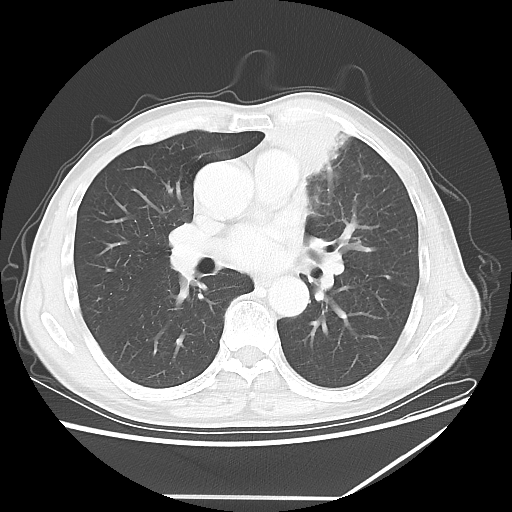
Chest CT, one axial slice; position 33 of 64 along the scan axis; 100 kVp; lung window (W 1500 / L -600 HU); 5 mm slice thickness; 512 × 512 image matrix, field of view 383 × 383 mm. Male patient, age 64 years. Case-level facts recorded for this patient, not image findings: clinical TNM (as recorded): T1c N1 M1.
Structures marked on this image (bounding box drawn by a radiologist):
- lung tumour (recorded histology: squamous cell carcinoma): box from (x=225, y=92) to (x=363, y=197) px